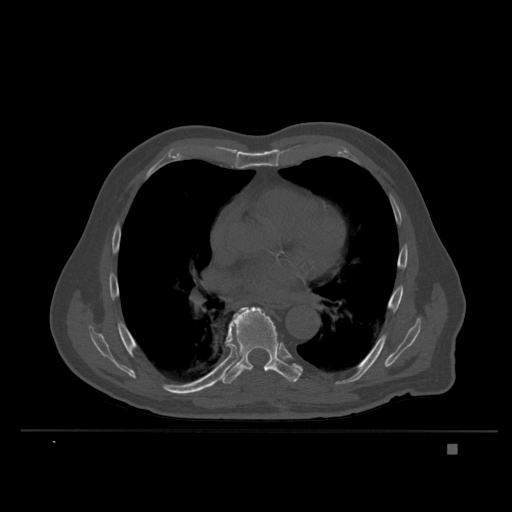
CT including the spine, one axial slice; slice 234 of 435 in the series (ordered by position); bone window (W 1800 / L 400 HU); 1.5 mm slice thickness; 512 × 512 image matrix, field of view 434 × 434 mm. Male patient, age 73 years. Case-level facts recorded for this patient, not image findings: primary cancer: skin.
Annotated regions visible in this slice (semi-automatic segmentation, software-assisted and operator-edited):
- T7 vertebra: bounding box <226,321,233,342> (left, top, right, bottom; pixels)
- T8 vertebra: <219,307,301,384>